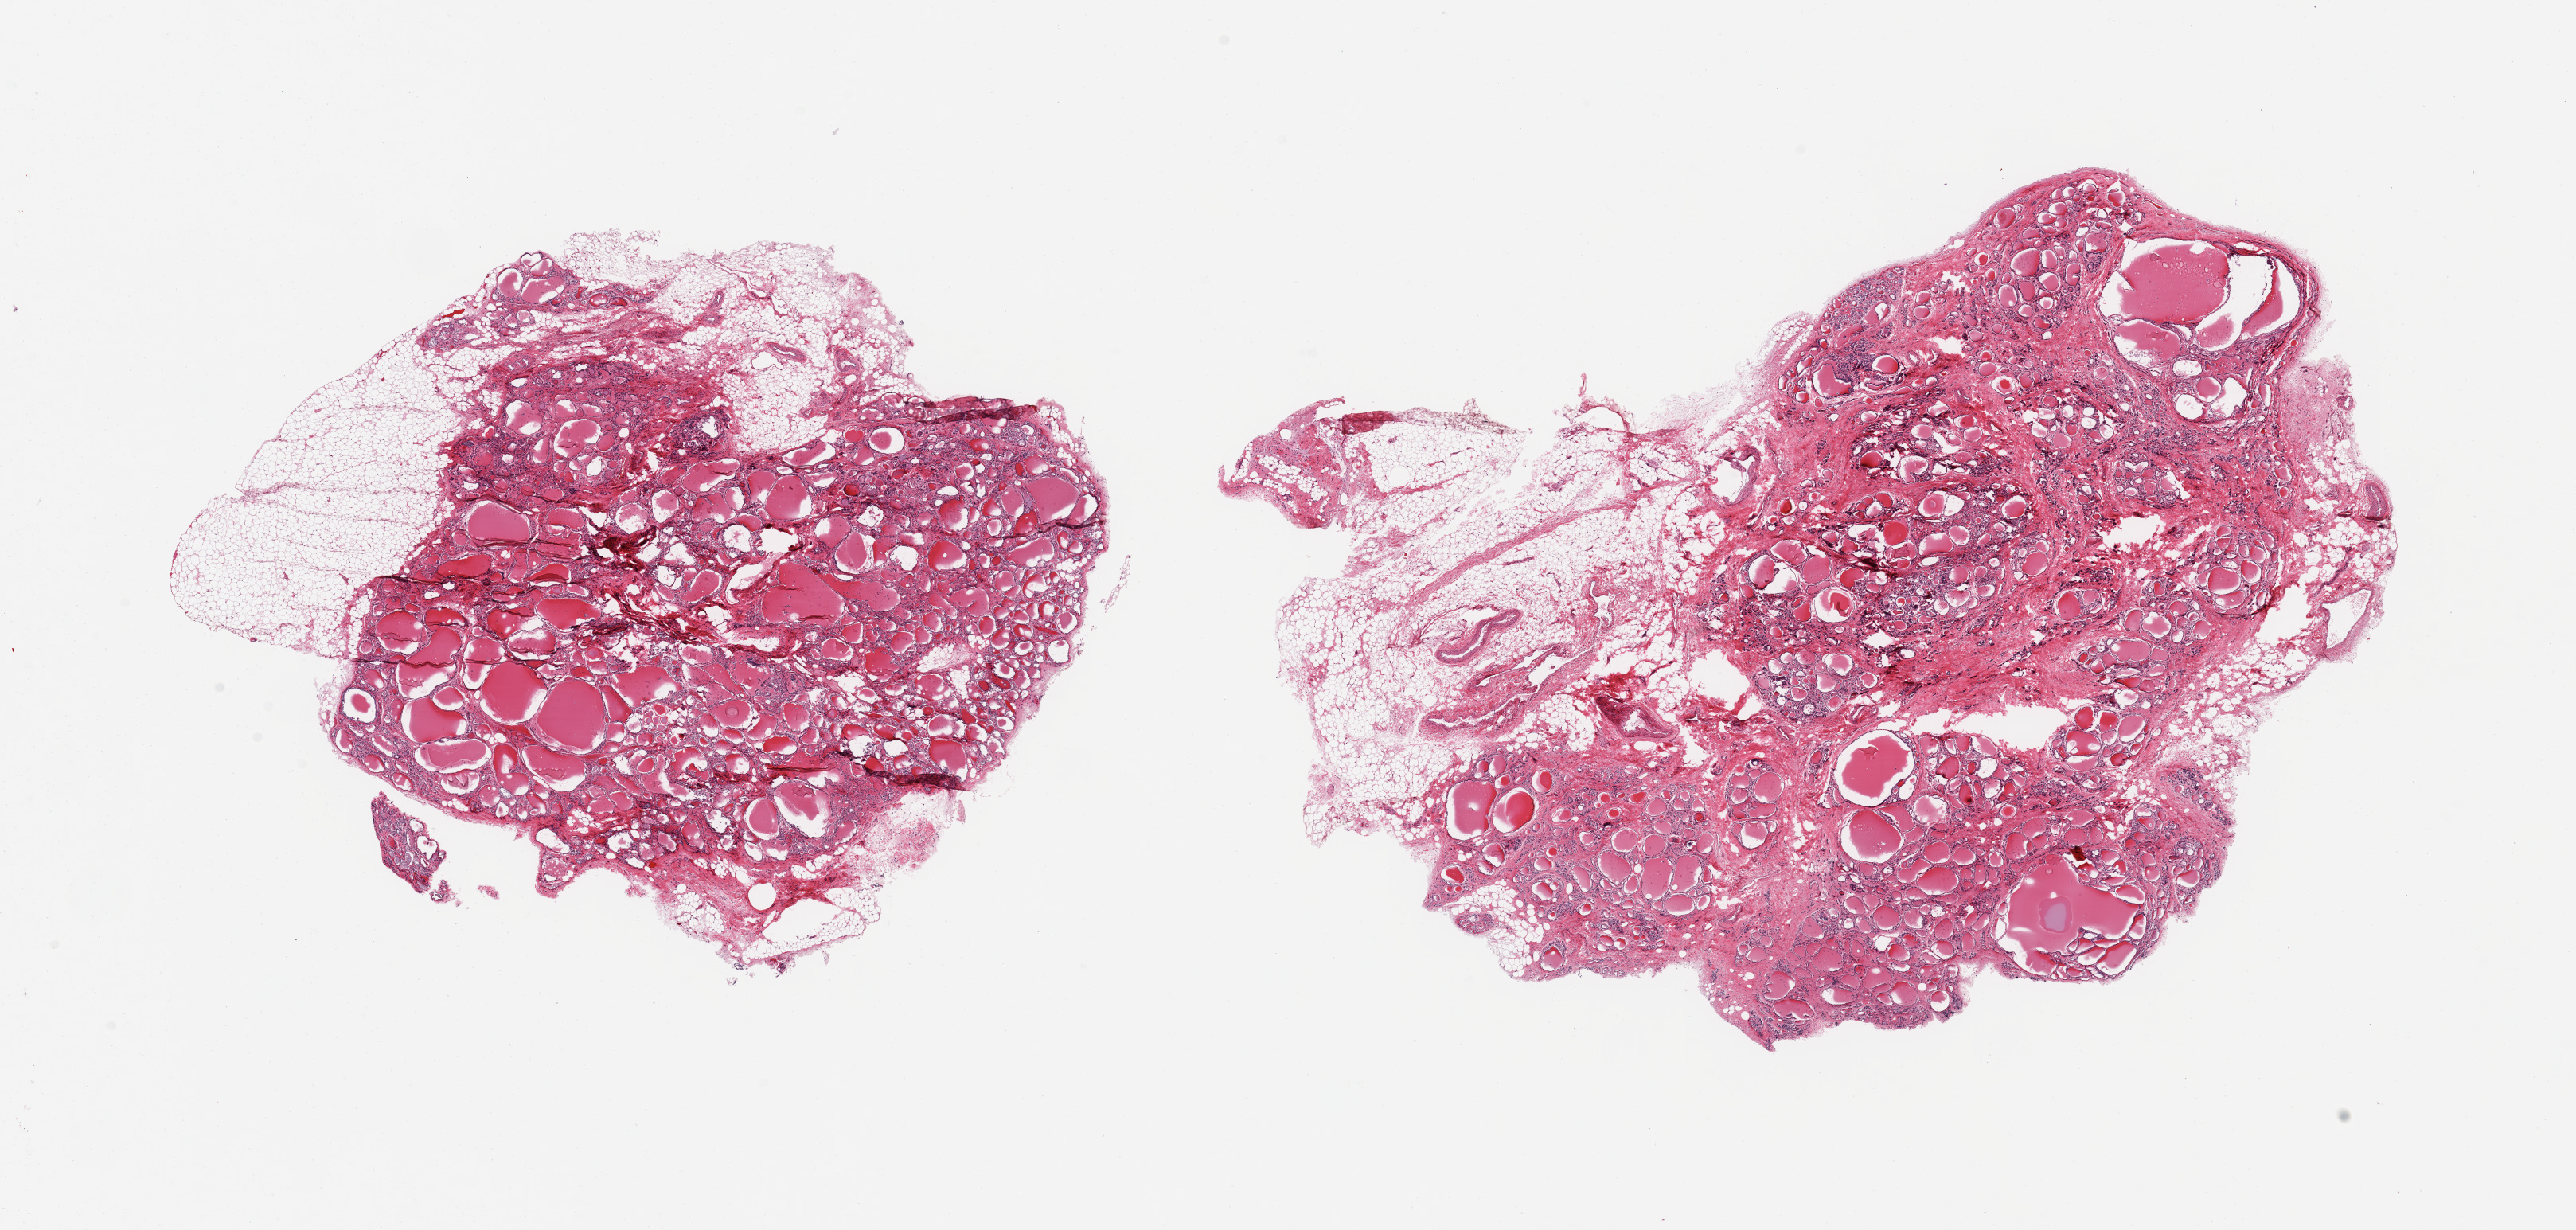
Whole-slide image, H&E stain, brightfield — whole scanned area (about 25.6 x 12.2 mm) shown as a low-resolution overview. PAXgene-fixed, paraffin-embedded tissue. Sampled site (target tissue): thyroid. Tissue donor sample. Female donor.
- pathologist's review note for this sample: 2 pieces, nodular goitre; regressive changes; adherent nubbins of fat up to ~3mm